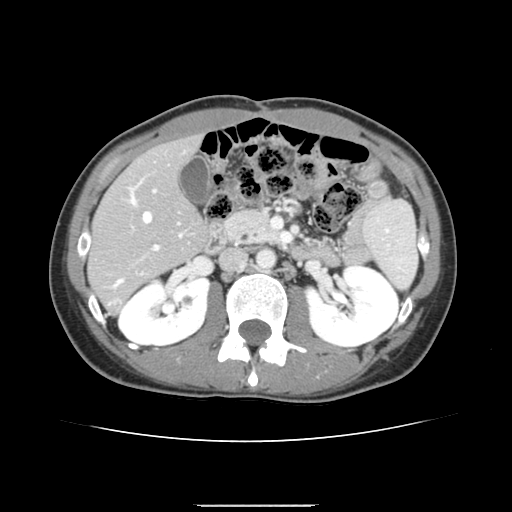
Contrast-enhanced abdominal CT, one axial slice; slice 71 of 150 in the series (ordered by position); 120 kVp; intravenous contrast given; soft-tissue window (W 400 / L 40 HU); 2.5 mm slice thickness; 512 × 512 image matrix. Female patient, age 32 years. Case-level facts recorded for this patient, not image findings: diagnosis: colorectal cancer liver metastases, imaged before liver resection; multiple liver metastases: yes.
Outlined on this slice (outlined manually by an expert reader):
- hepatic veins: box from (x=115, y=192) to (x=181, y=286) px
- liver: (x=90, y=138)–(x=206, y=311)
- planned liver remnant (the part of the liver to remain after resection): (x=90, y=138)–(x=206, y=285)
- portal vein (with intrahepatic branches): (x=111, y=183)–(x=159, y=304)